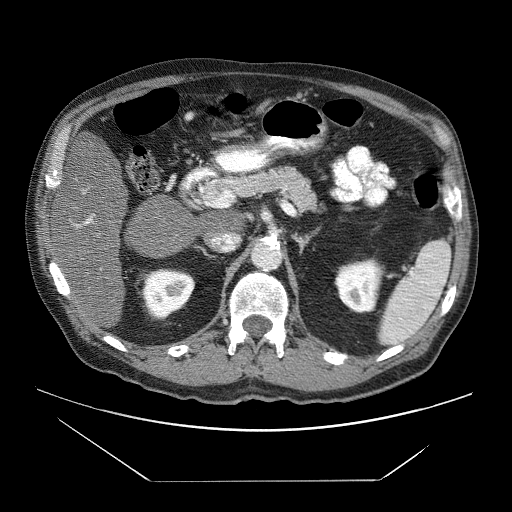
Contrast-enhanced abdominal CT (liver protocol), one axial slice; slice 28 of 83 in the series (ordered by position); soft-tissue window (W 400 / L 40 HU); 512 × 512 image matrix. Case-level facts recorded for this patient, not image findings: diagnosis: hepatocellular carcinoma (patient treated with transarterial chemoembolisation; whether this scan precedes or follows treatment is not stated here); TNM stage (as recorded): Stage-IVB; Child-Pugh class: B; tumour differentiation: poorly differentiated; tumour nodularity: uninodular.
Outlined on this slice (semi-automatically segmented with operator editing):
- liver parenchyma outside the tumour (the mass and vessels are separate outlines, so this box may not span the whole liver): bounding box [x1, y1, x2, y2] px = [53, 153, 126, 330]
- liver vessels: [73, 191, 94, 227]